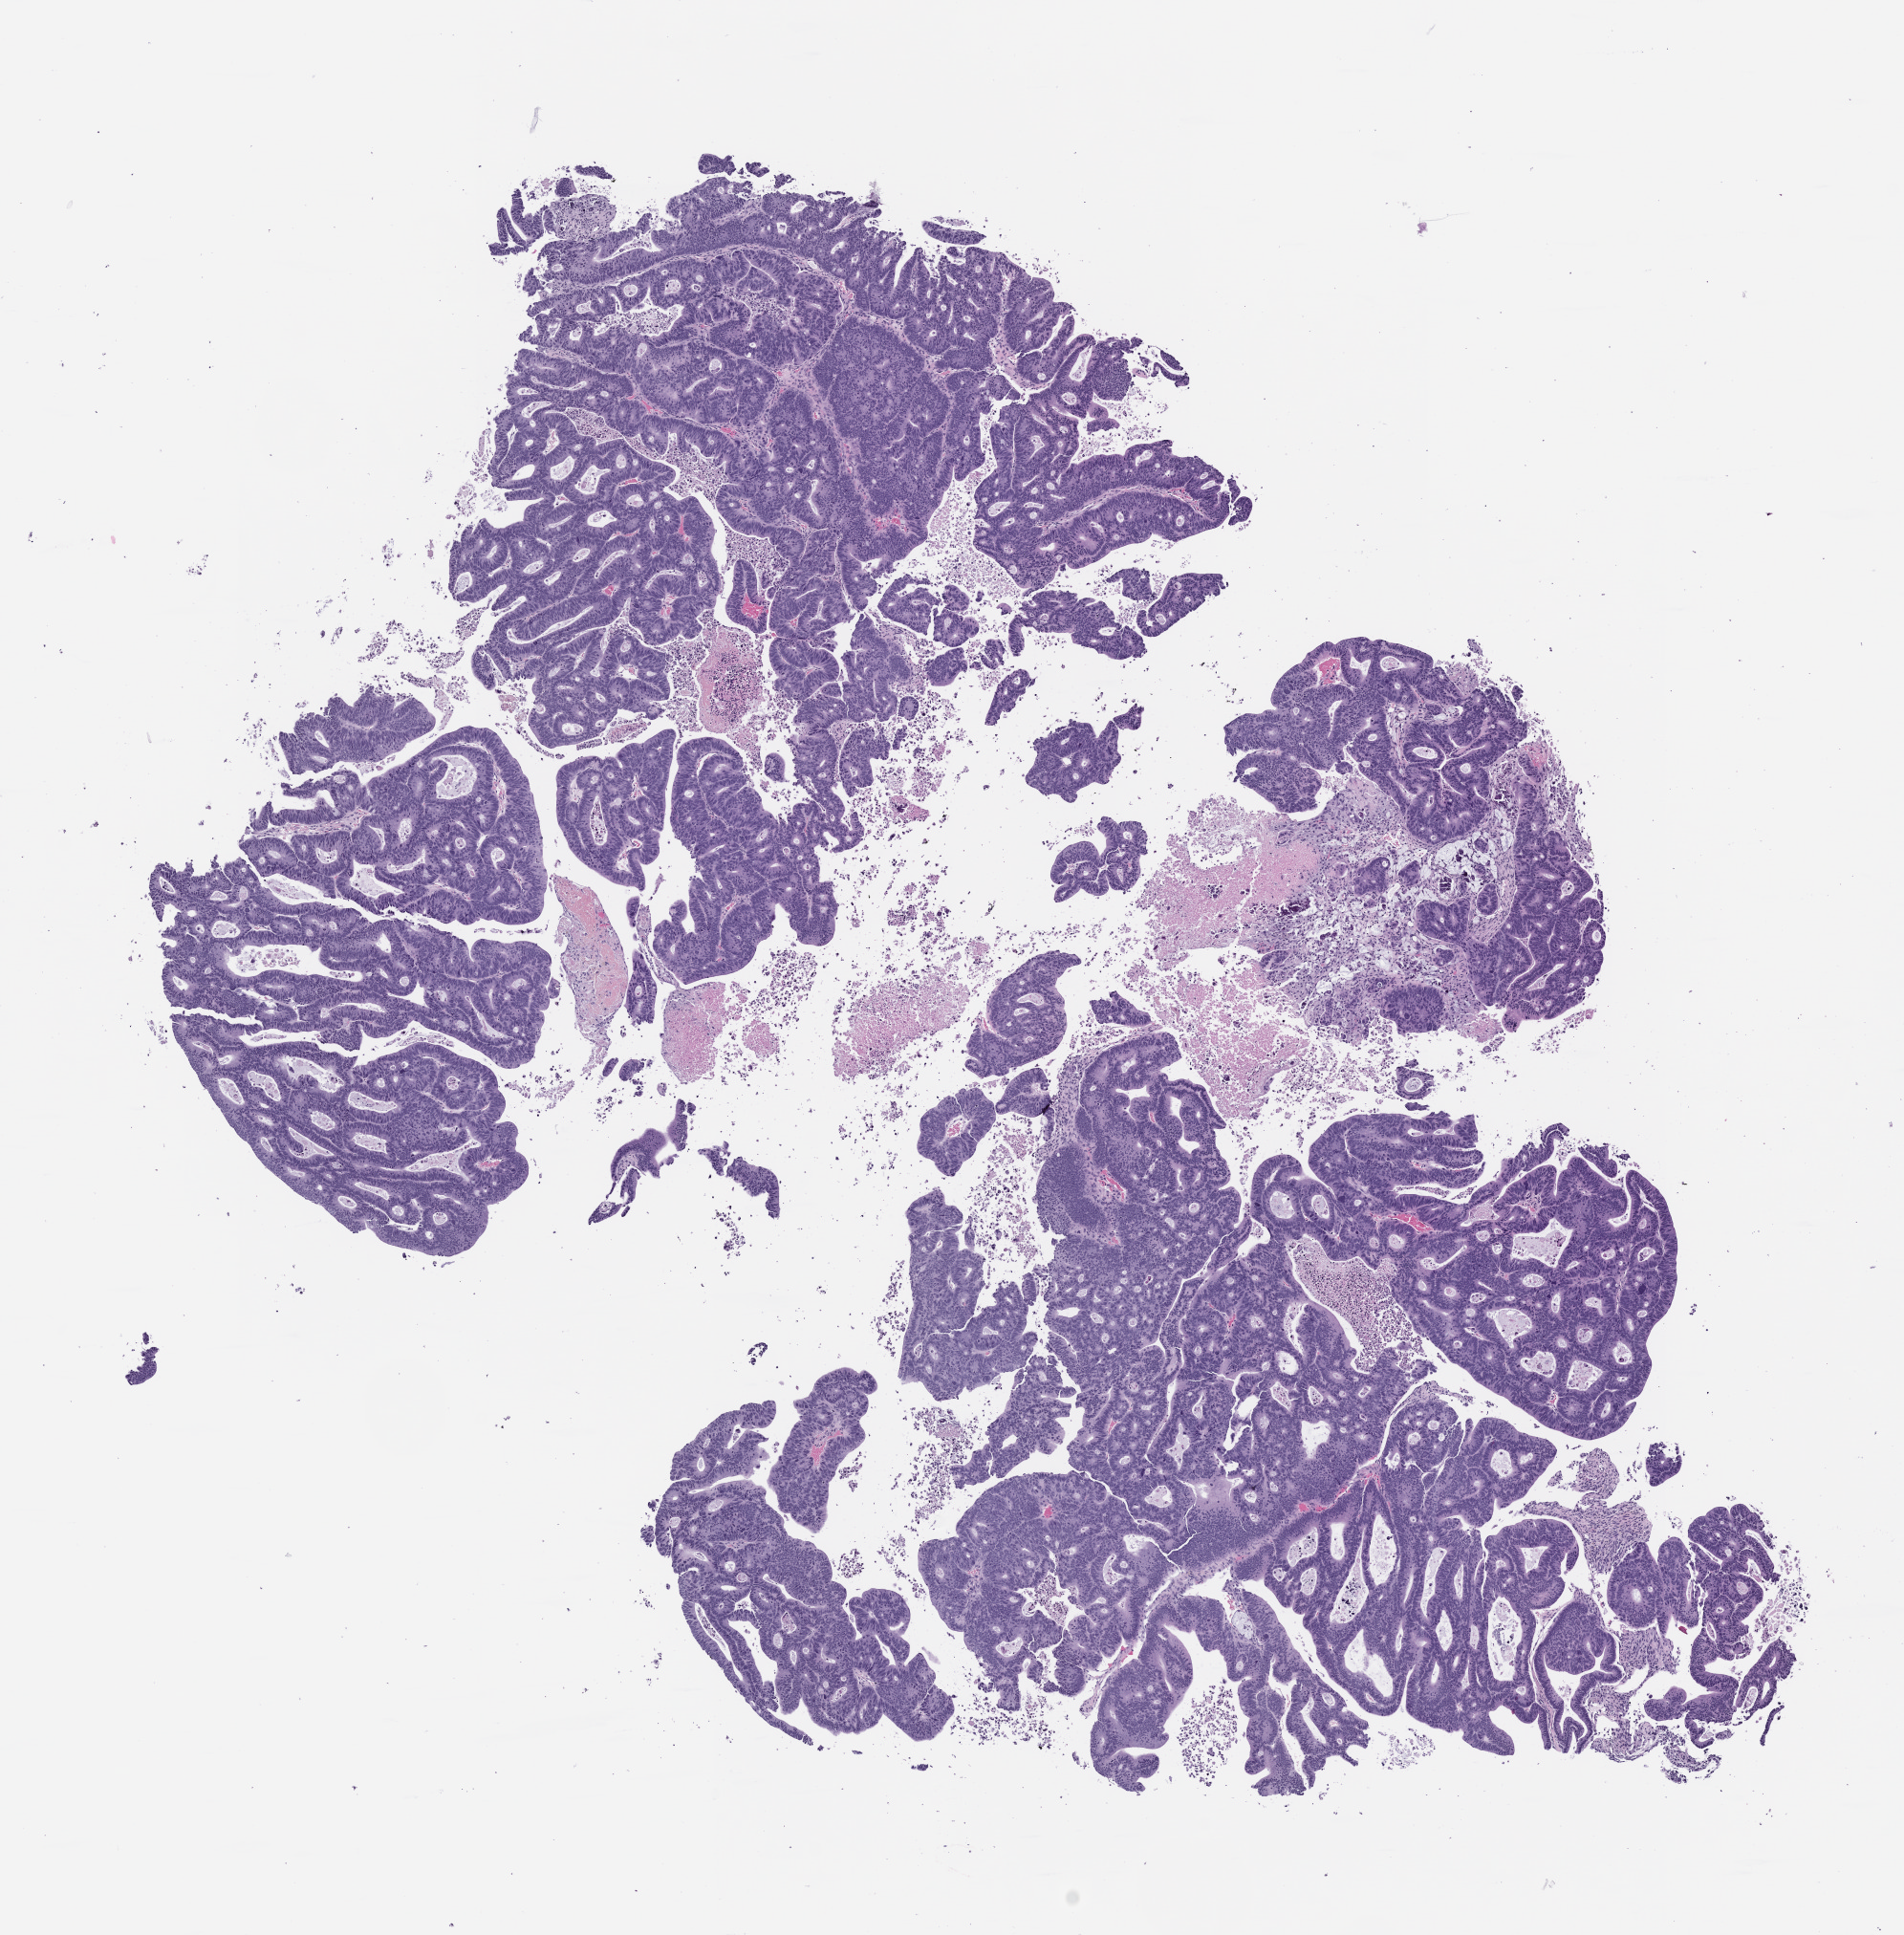
Haematoxylin and eosin whole-slide image of a patient-derived xenograft (PDX) tumor grown in a mouse, passage 1 — shown as a low-resolution overview of the whole scanned area (about 8.0 x 8.1 mm); formalin-fixed, paraffin-embedded (FFPE) tissue; tumor site category: colon.
- originating patient diagnosis: Colon Adenocarcinoma